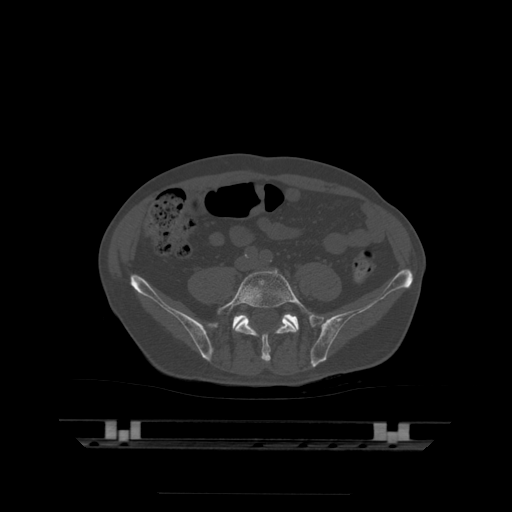
CT including the spine, one axial slice. Slice 70 of 522 in the series (ordered by position). Bone window (W 1800 / L 400 HU). 1.25 mm slice thickness. 512 × 512 image matrix, field of view 436 × 436 mm. Patient age 68 years. Case-level facts recorded for this patient, not image findings: primary cancer: urothelial.
Annotated regions visible in this slice (semi-automatic segmentation, software-assisted and operator-edited):
- L5 vertebra: bounding box <217,269,313,362> (left, top, right, bottom; pixels)